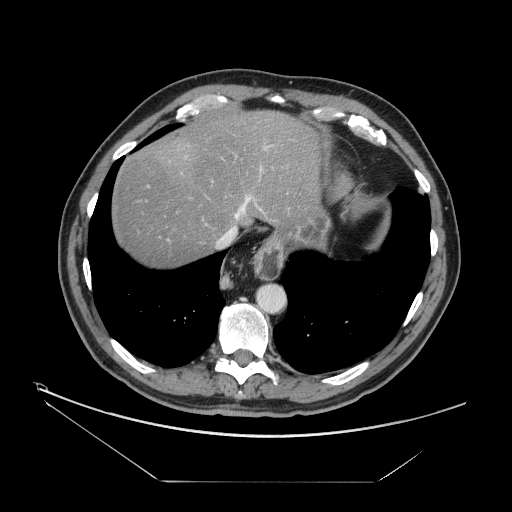
Contrast-enhanced abdominal CT, one axial slice. Slice 136 of 161 in the series (ordered by position). 120 kVp. Intravenous contrast given. Soft-tissue window (W 400 / L 40 HU). 512 × 512 image matrix, field of view 440 × 440 mm. Male patient, age 65 years. From the clinical record (not read from this slice): diagnosis: colorectal cancer liver metastases, imaged before liver resection; multiple liver metastases: yes; largest metastasis: 4.2 cm; chemotherapy before resection: yes.
Outlined on this slice (expert manual segmentation):
- hepatic veins: bounding box <215,191,253,249> (left, top, right, bottom; pixels)
- liver: <111,108,320,266>
- planned liver remnant (the part of the liver to remain after resection): <111,108,320,267>
- portal vein (with intrahepatic branches): <148,146,267,241>